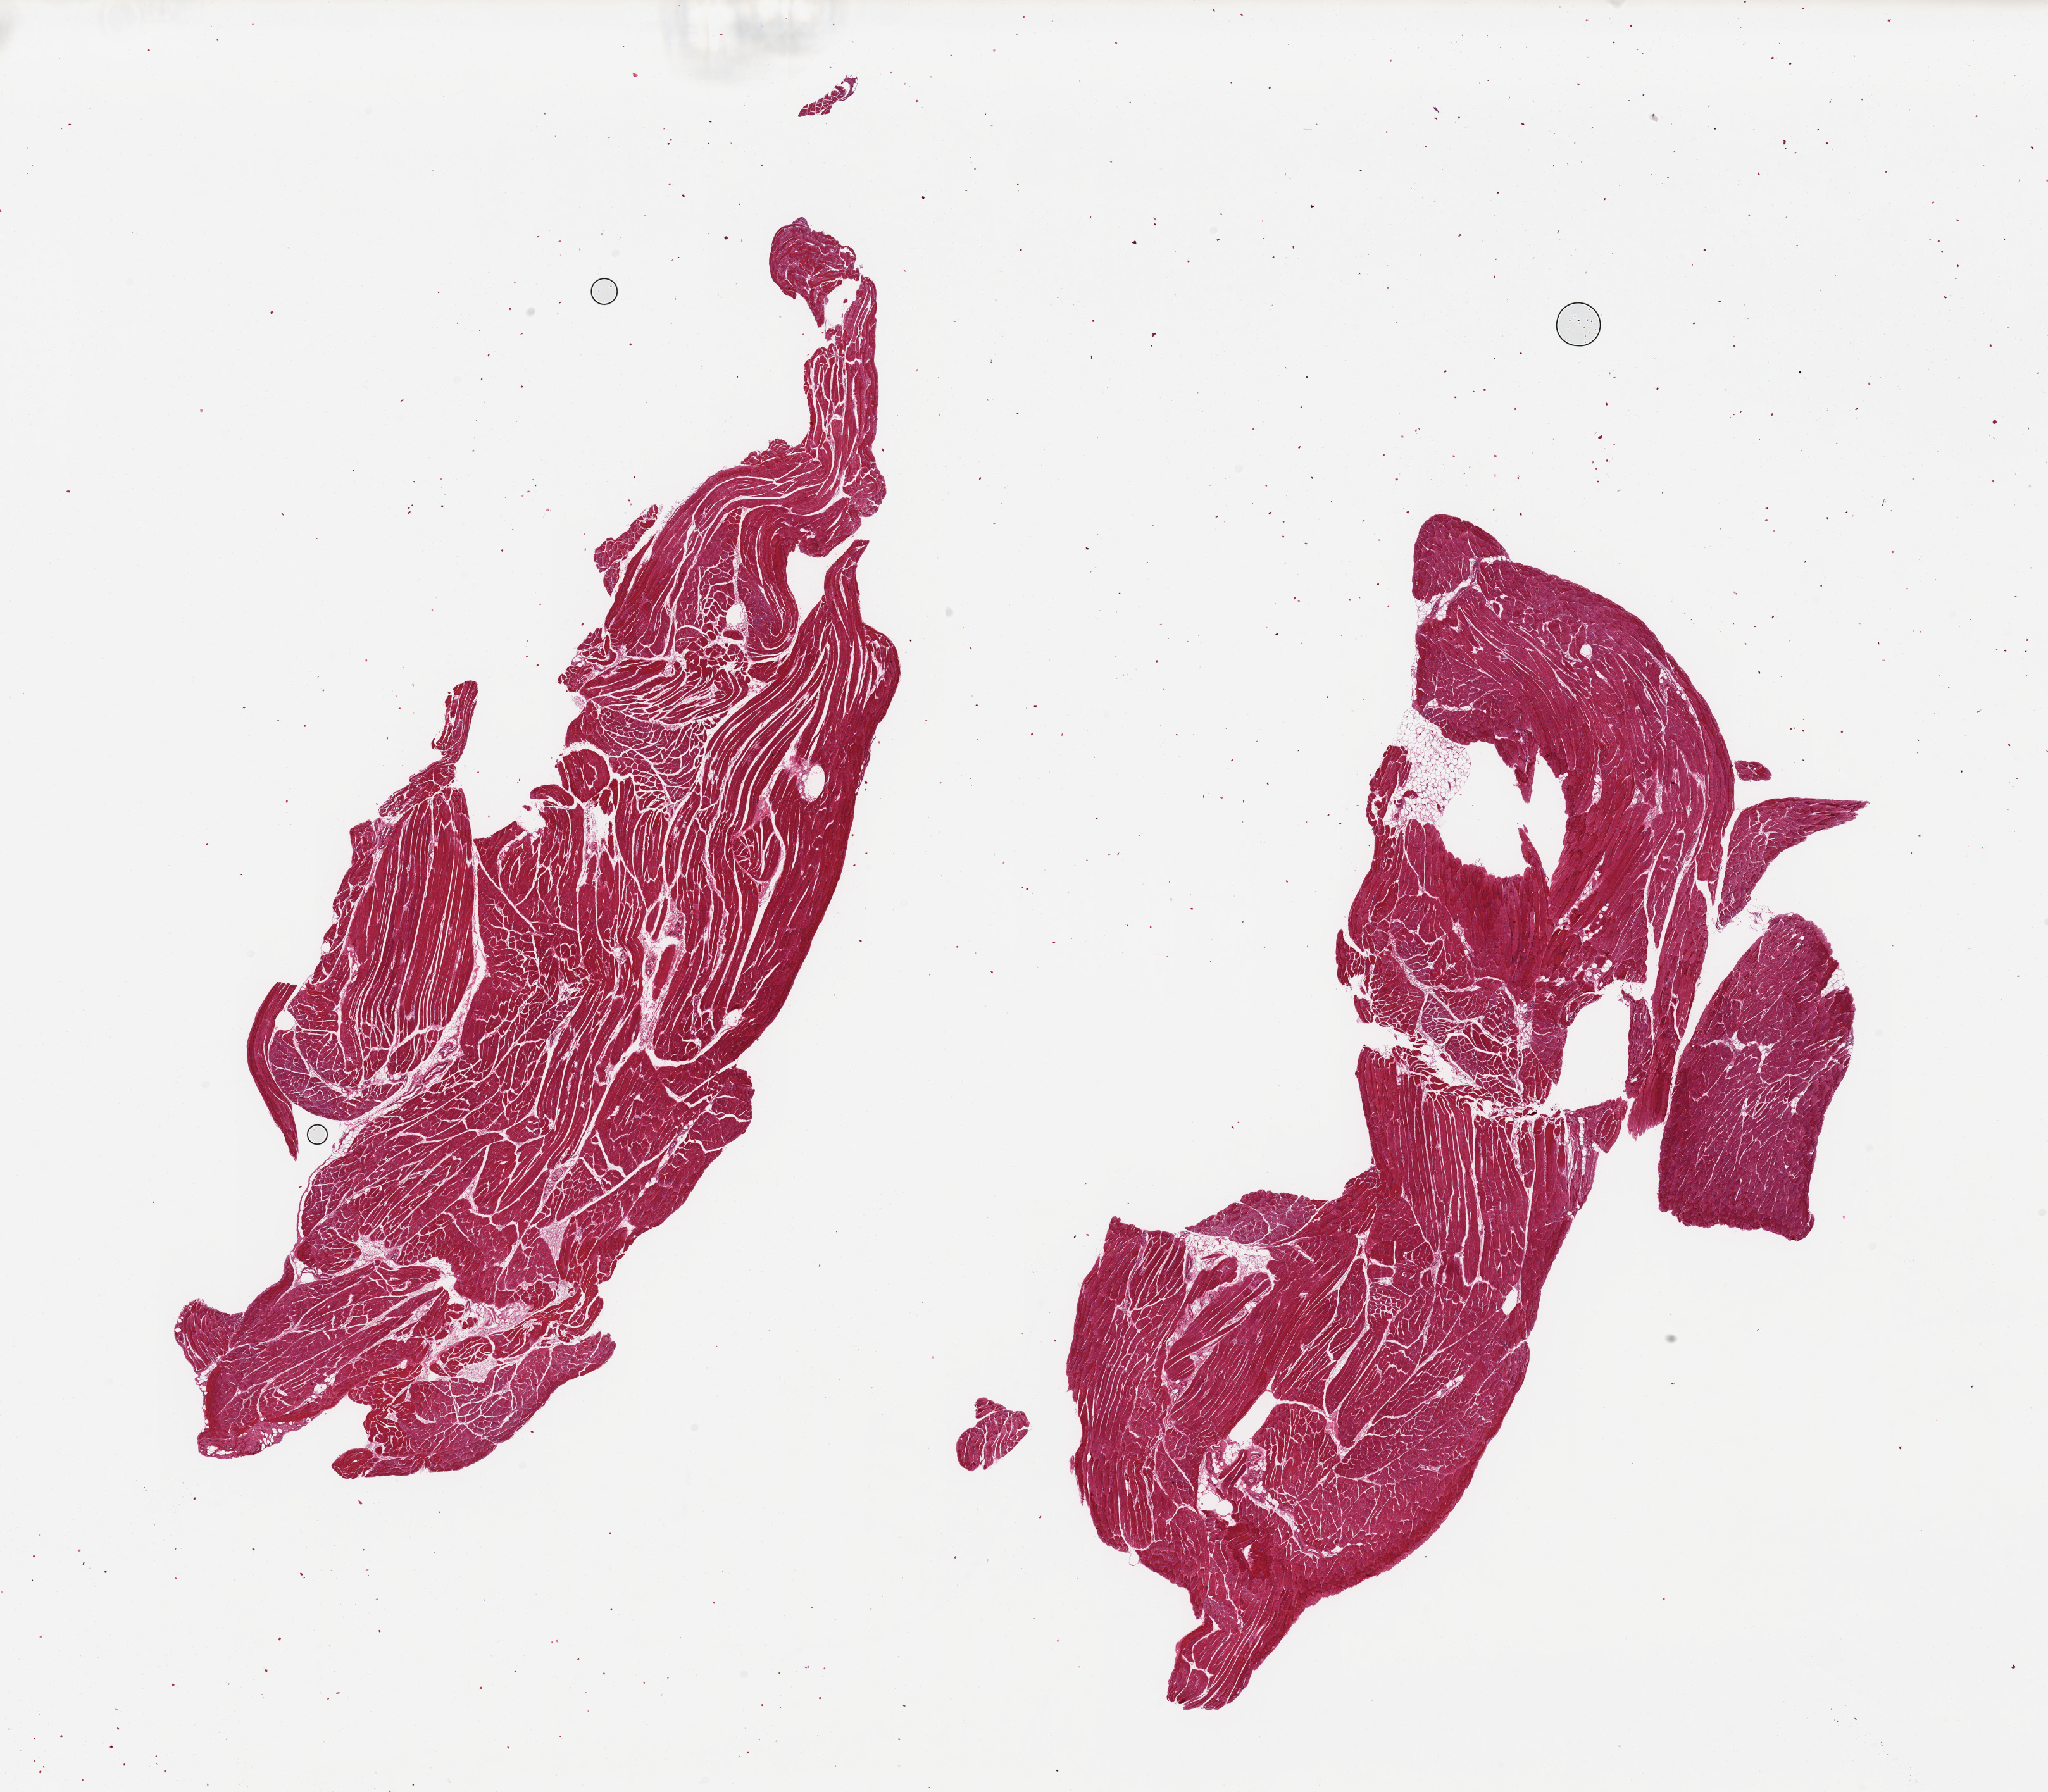
Digitized H&E-stained section, shown as a low-resolution overview of the whole scanned area (about 25.6 x 22.4 mm, from a 20x scan), PAXgene-fixed, paraffin-embedded tissue, sampled site (target tissue): skeletal muscle, donor tissue sample. Donor: male.
Review note (as recorded): 2 pieces, ~5% interstitial fat.